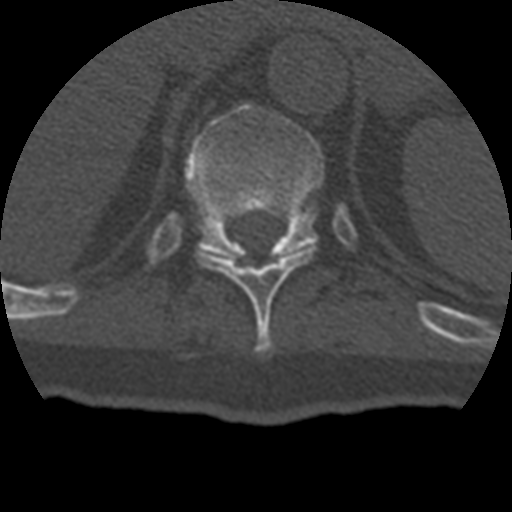
CT including the spine, one axial slice. Position 208 of 399 along the scan axis. 120 kVp. Bone window (W 1800 / L 400 HU). 1.25 mm slice thickness. 512 × 512 image matrix. Patient age 69 years. From the clinical record (not read from this slice): primary cancer: prostate.
Outlined on this slice (semi-automatic segmentation, software-assisted and operator-edited):
- T10 vertebra: box from (x=197, y=247) to (x=314, y=354) px
- T11 vertebra: (x=185, y=104)–(x=324, y=260)